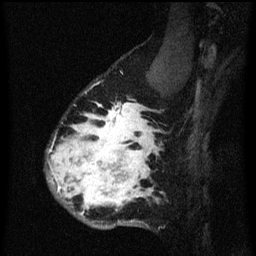
Breast MRI (dynamic contrast-enhanced), one sagittal slice. Position 48 of 60 along the scan axis. Dynamic contrast-enhanced series, image 2 of 3 at this slice position (ordered by acquisition). 1.5 T. TE 4.2 ms, TR 8.4 ms. 256 × 256 image matrix, field of view 180 × 180 mm. Patient: female, 34 years. Case-level facts recorded for this patient, not image findings: setting: breast cancer imaged before/during neoadjuvant chemotherapy; receptor status: HR-positive, HER2-negative.
Structures marked on this image (semi-automatic segmentation, software-assisted and operator-edited):
- analysis volume of interest (the breast-tissue region the enhancement analysis was run in; not a lesion): bounding box [x1, y1, x2, y2] px = [46, 58, 173, 231]
- tumour enhancement mask (voxels above the 70 % enhancement threshold inside the analysis volume of interest): [48, 102, 157, 215]